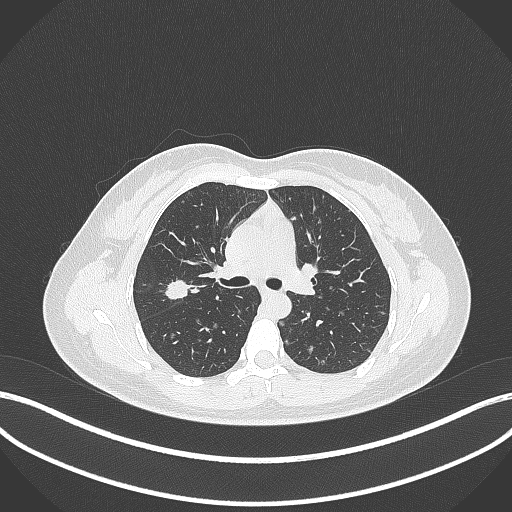
Chest CT, one axial slice. Position 212 of 307 along the scan axis. Reconstruction kernel B70f. Lung window (W 1500 / L -600 HU). 1 mm slice thickness. 512 × 512 image matrix, field of view 400 × 400 mm. Female patient, age 33 years. Case-level facts recorded for this patient, not image findings: clinical TNM (as recorded): T1c N0 M0.
Structures marked on this image (bounding box drawn by a radiologist):
- lung tumour (recorded histology: adenocarcinoma): bounding box [x1, y1, x2, y2] px = [164, 278, 189, 303]